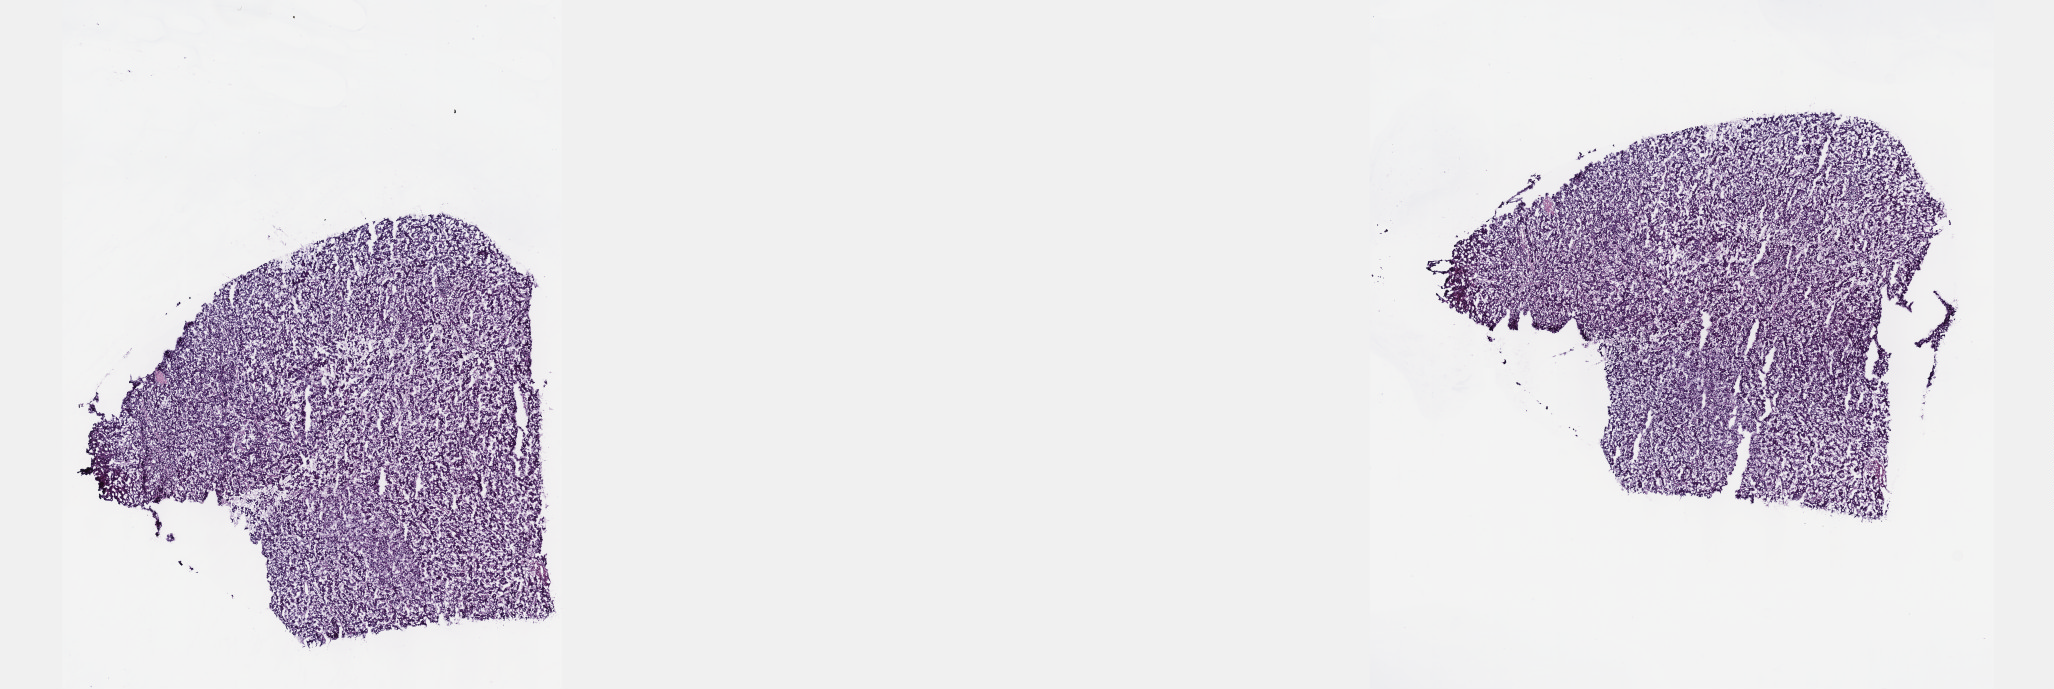
Digitized Hematoxylin and eosin (H&E) stained tissue section (whole slide), a low-resolution overview of the entire scanned area, about 16.6 x 5.6 mm (acquisition: 40x scan); frozen section from the top of the tissue portion; recurrent tumour sample from the liver. Male patient; age at initial diagnosis 64 years. Composition of this section per pathologist review: tumour cells 100%, tumour nuclei 80%, normal cells 0%, stromal cells 0%, necrosis 0%. Inflammatory infiltration, as recorded: lymphocyte infiltration 2%, monocyte infiltration 0%, neutrophil infiltration 0%.
This section: recurrent tumour. Patient diagnosis: Hepatocellular carcinoma, NOS.